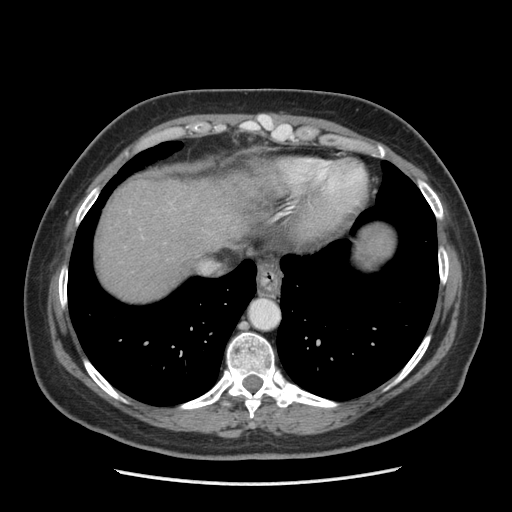
Contrast-enhanced abdominal CT (liver protocol), one axial slice. Position 171 of 185 along the scan axis. Reconstruction kernel STANDARD. Soft-tissue window (W 400 / L 40 HU). 512 × 512 image matrix, field of view 360 × 360 mm. From the clinical record (not read from this slice): diagnosis: hepatocellular carcinoma (patient treated with transarterial chemoembolisation; whether this scan precedes or follows treatment is not stated here); TNM stage (as recorded): Stage-I; Child-Pugh class: A; tumour nodularity: uninodular.
Outlined on this slice (semi-automatically segmented with operator editing):
- liver parenchyma outside the tumour (the mass and vessels are separate outlines, so this box may not span the whole liver): box from (x=96, y=163) to (x=394, y=300) px